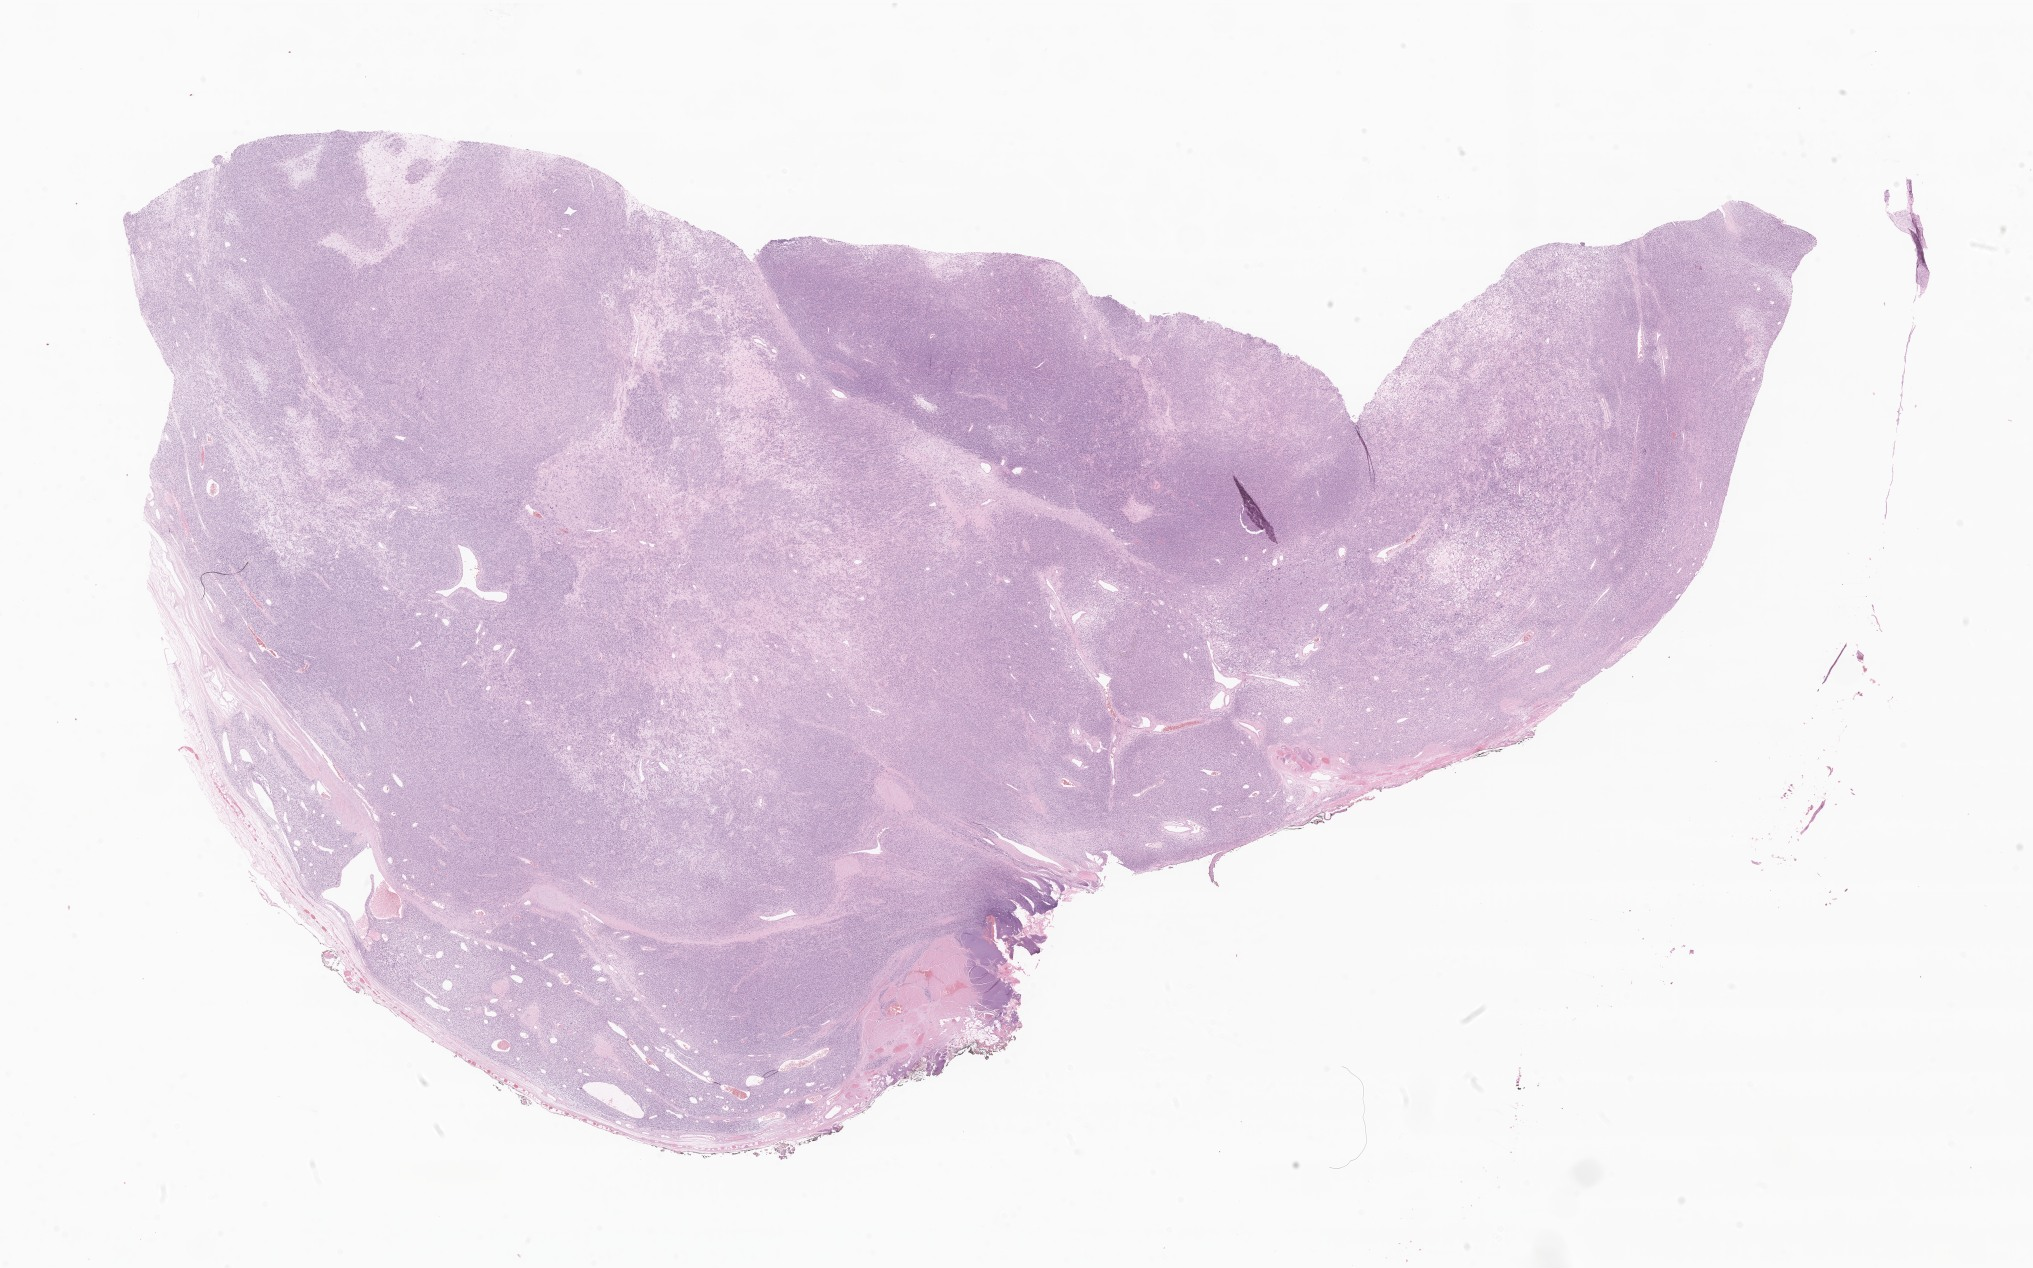
Hematoxylin and eosin (H&E) whole-slide image of tumor tissue from the soft tissue of trunk, whole scanned area (about 34.3 x 21.4 mm) shown as a low-resolution overview; formalin-fixed paraffin-embedded section. Patient: male, age 52 months (4 years 4 months).
* diagnosis: Embryonal rhabdomyosarcoma, NOS